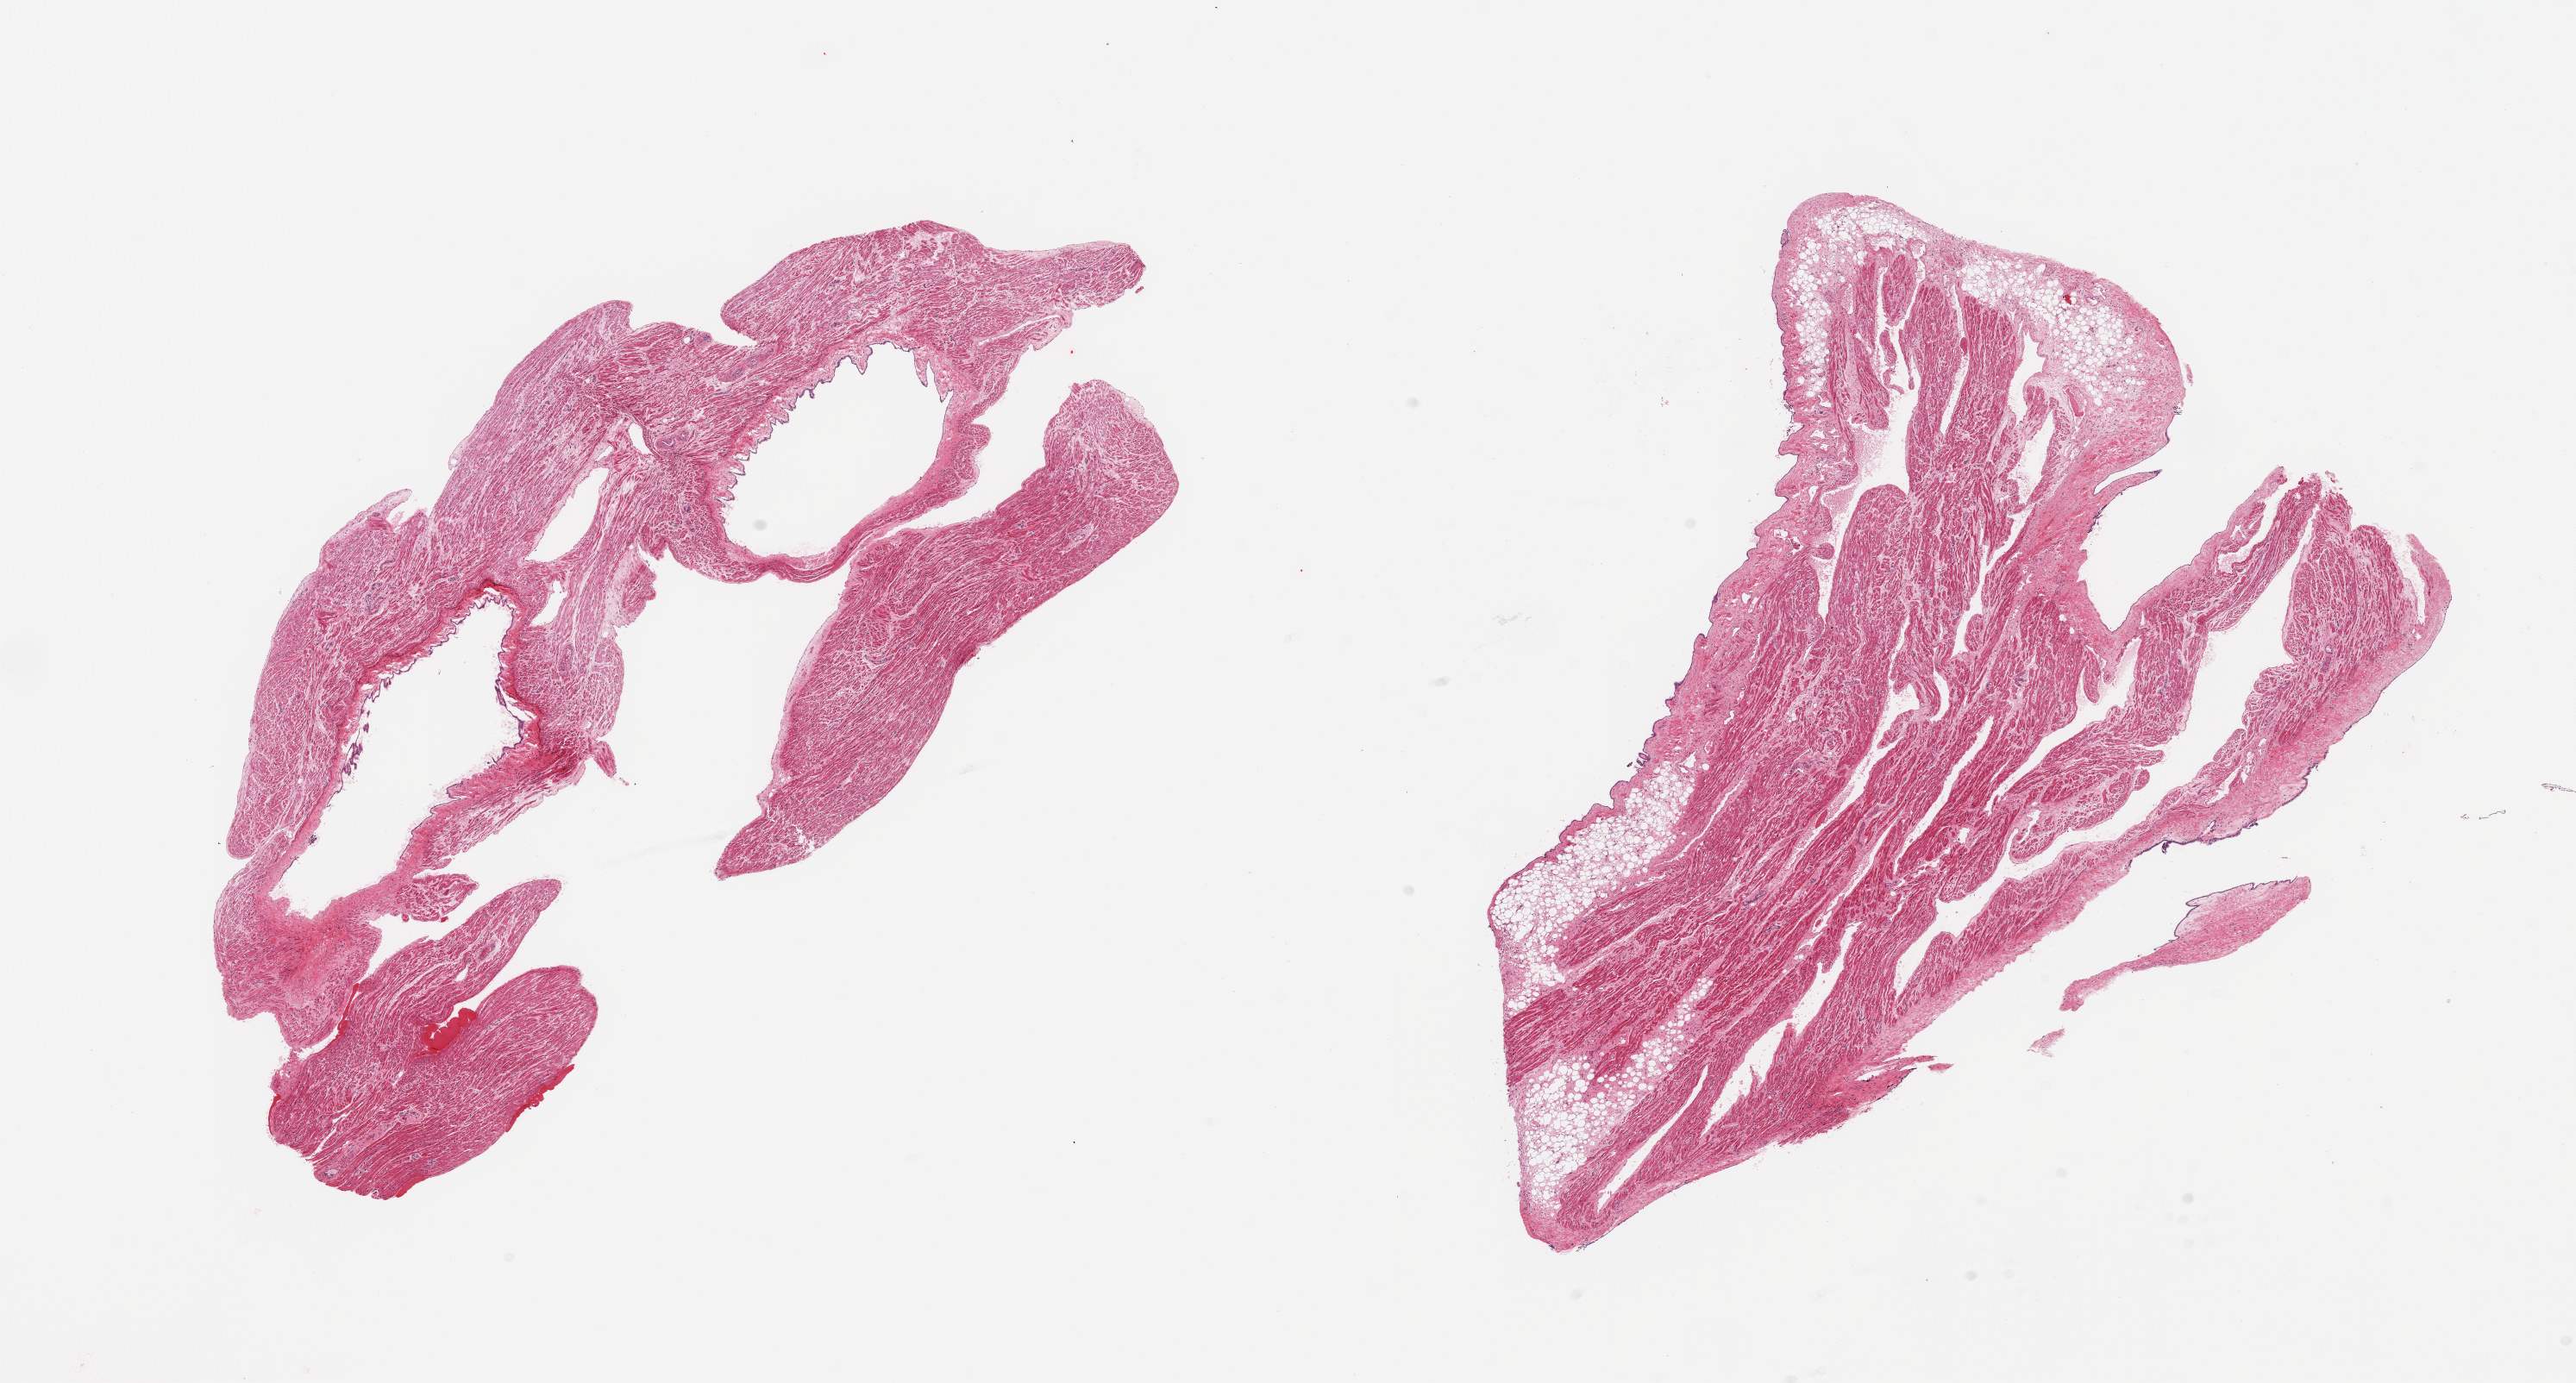
H&E whole-slide image, brightfield, whole scanned area (about 23.6 x 12.7 mm) shown as a low-resolution overview. PAXgene-fixed, paraffin-embedded tissue. Sampled site (target tissue): auricular appendage. Tissue donor sample. Donor sex: female.
Review note (as recorded): 2 pieces; 20%, mostly external, fat on 1 piece.